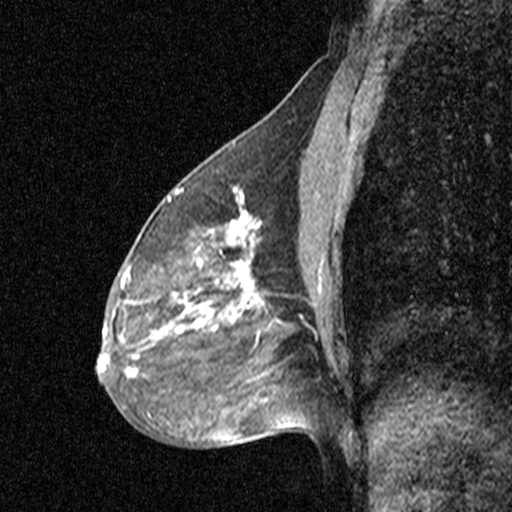
Breast MRI (dynamic contrast-enhanced), one sagittal slice; position 24 of 44 along the scan axis; dynamic contrast-enhanced study with each time point stored as its own series, time point 2 of 3 at this slice position (early post-contrast, ordered by acquisition time); 1.5 T; TE 4.5 ms, TR 11 ms; 3 mm slice thickness; 512 × 512 image matrix, field of view 200 × 200 mm. Female patient, age 53 years. Case-level facts recorded for this patient, not image findings: setting: breast cancer imaged before/during neoadjuvant chemotherapy; receptor status: HR-positive, HER2-negative.
Structures marked on this image (semi-automatic segmentation, software-assisted and operator-edited):
- analysis volume of interest (the breast-tissue region the enhancement analysis was run in; not a lesion): bounding box <88,176,313,423> (left, top, right, bottom; pixels)
- tumour enhancement mask (voxels above the 90 % enhancement threshold inside the analysis volume of interest): <100,191,300,377>